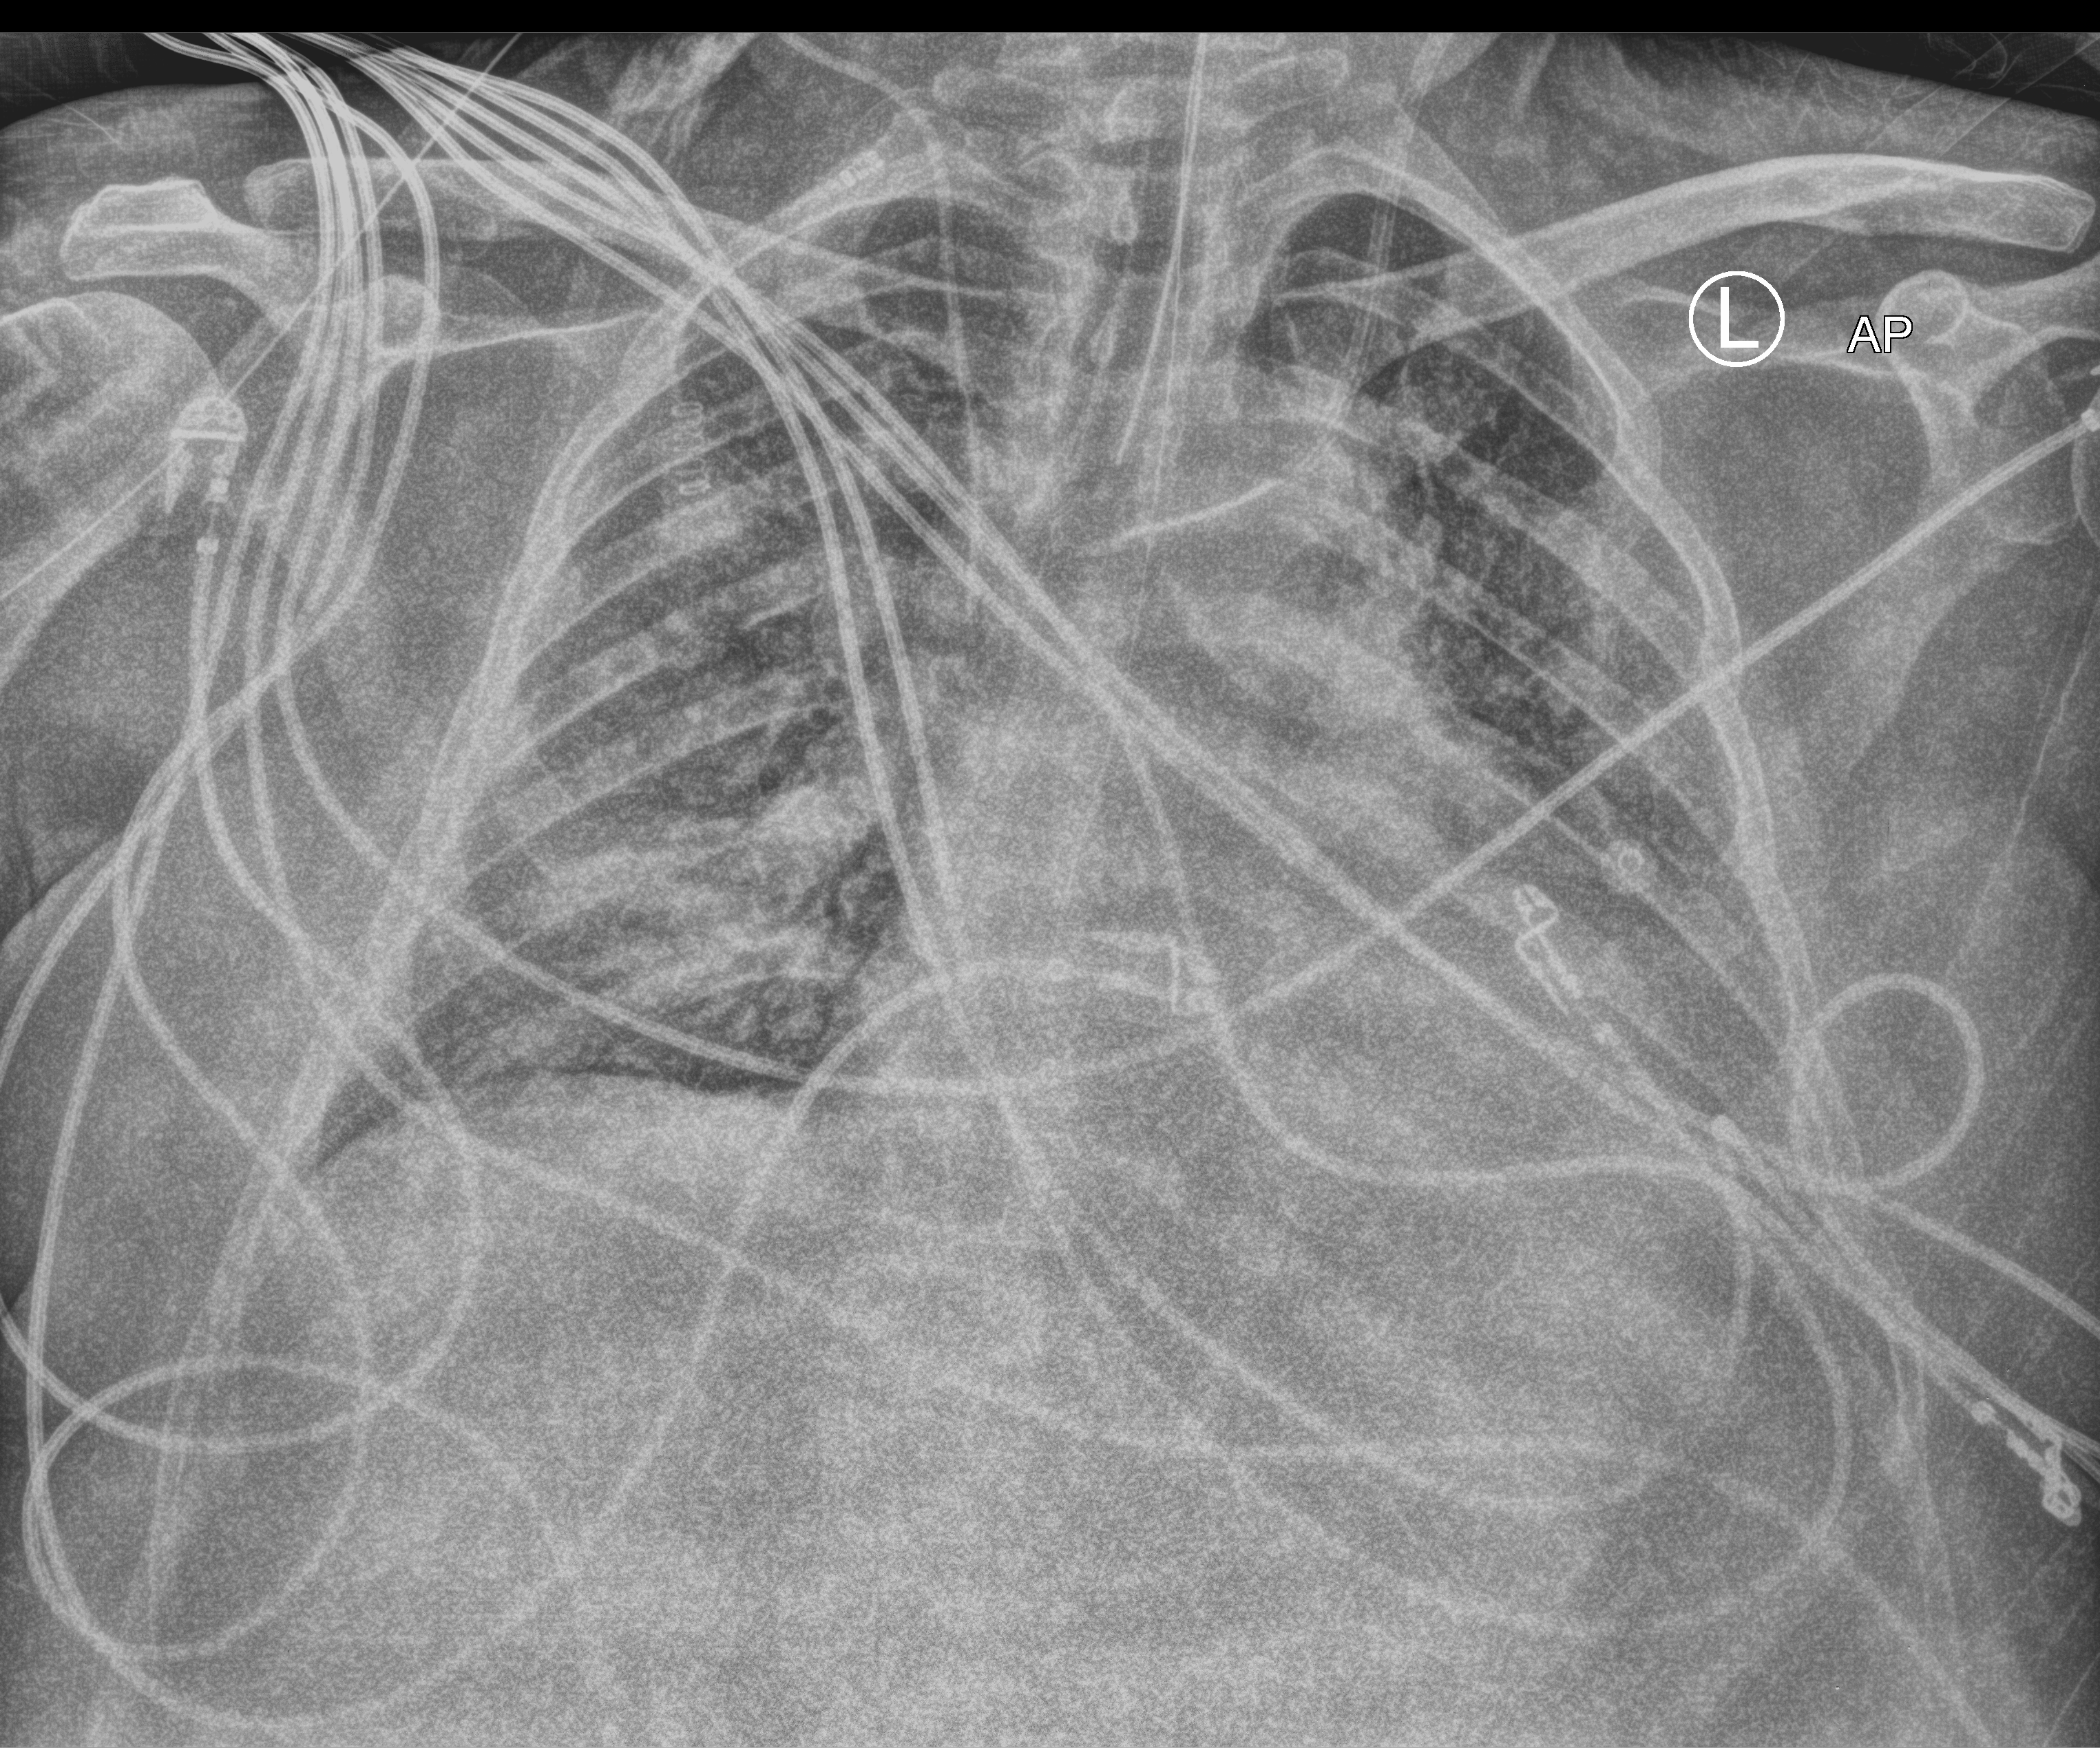
Bedside chest radiograph (computed radiography). Male patient hospitalised with COVID-19, age 18–59 years.
Hospital-stay facts (about this admission, not read from this image; timing relative to this image not recorded): admitted to intensive care during this hospital stay: yes.